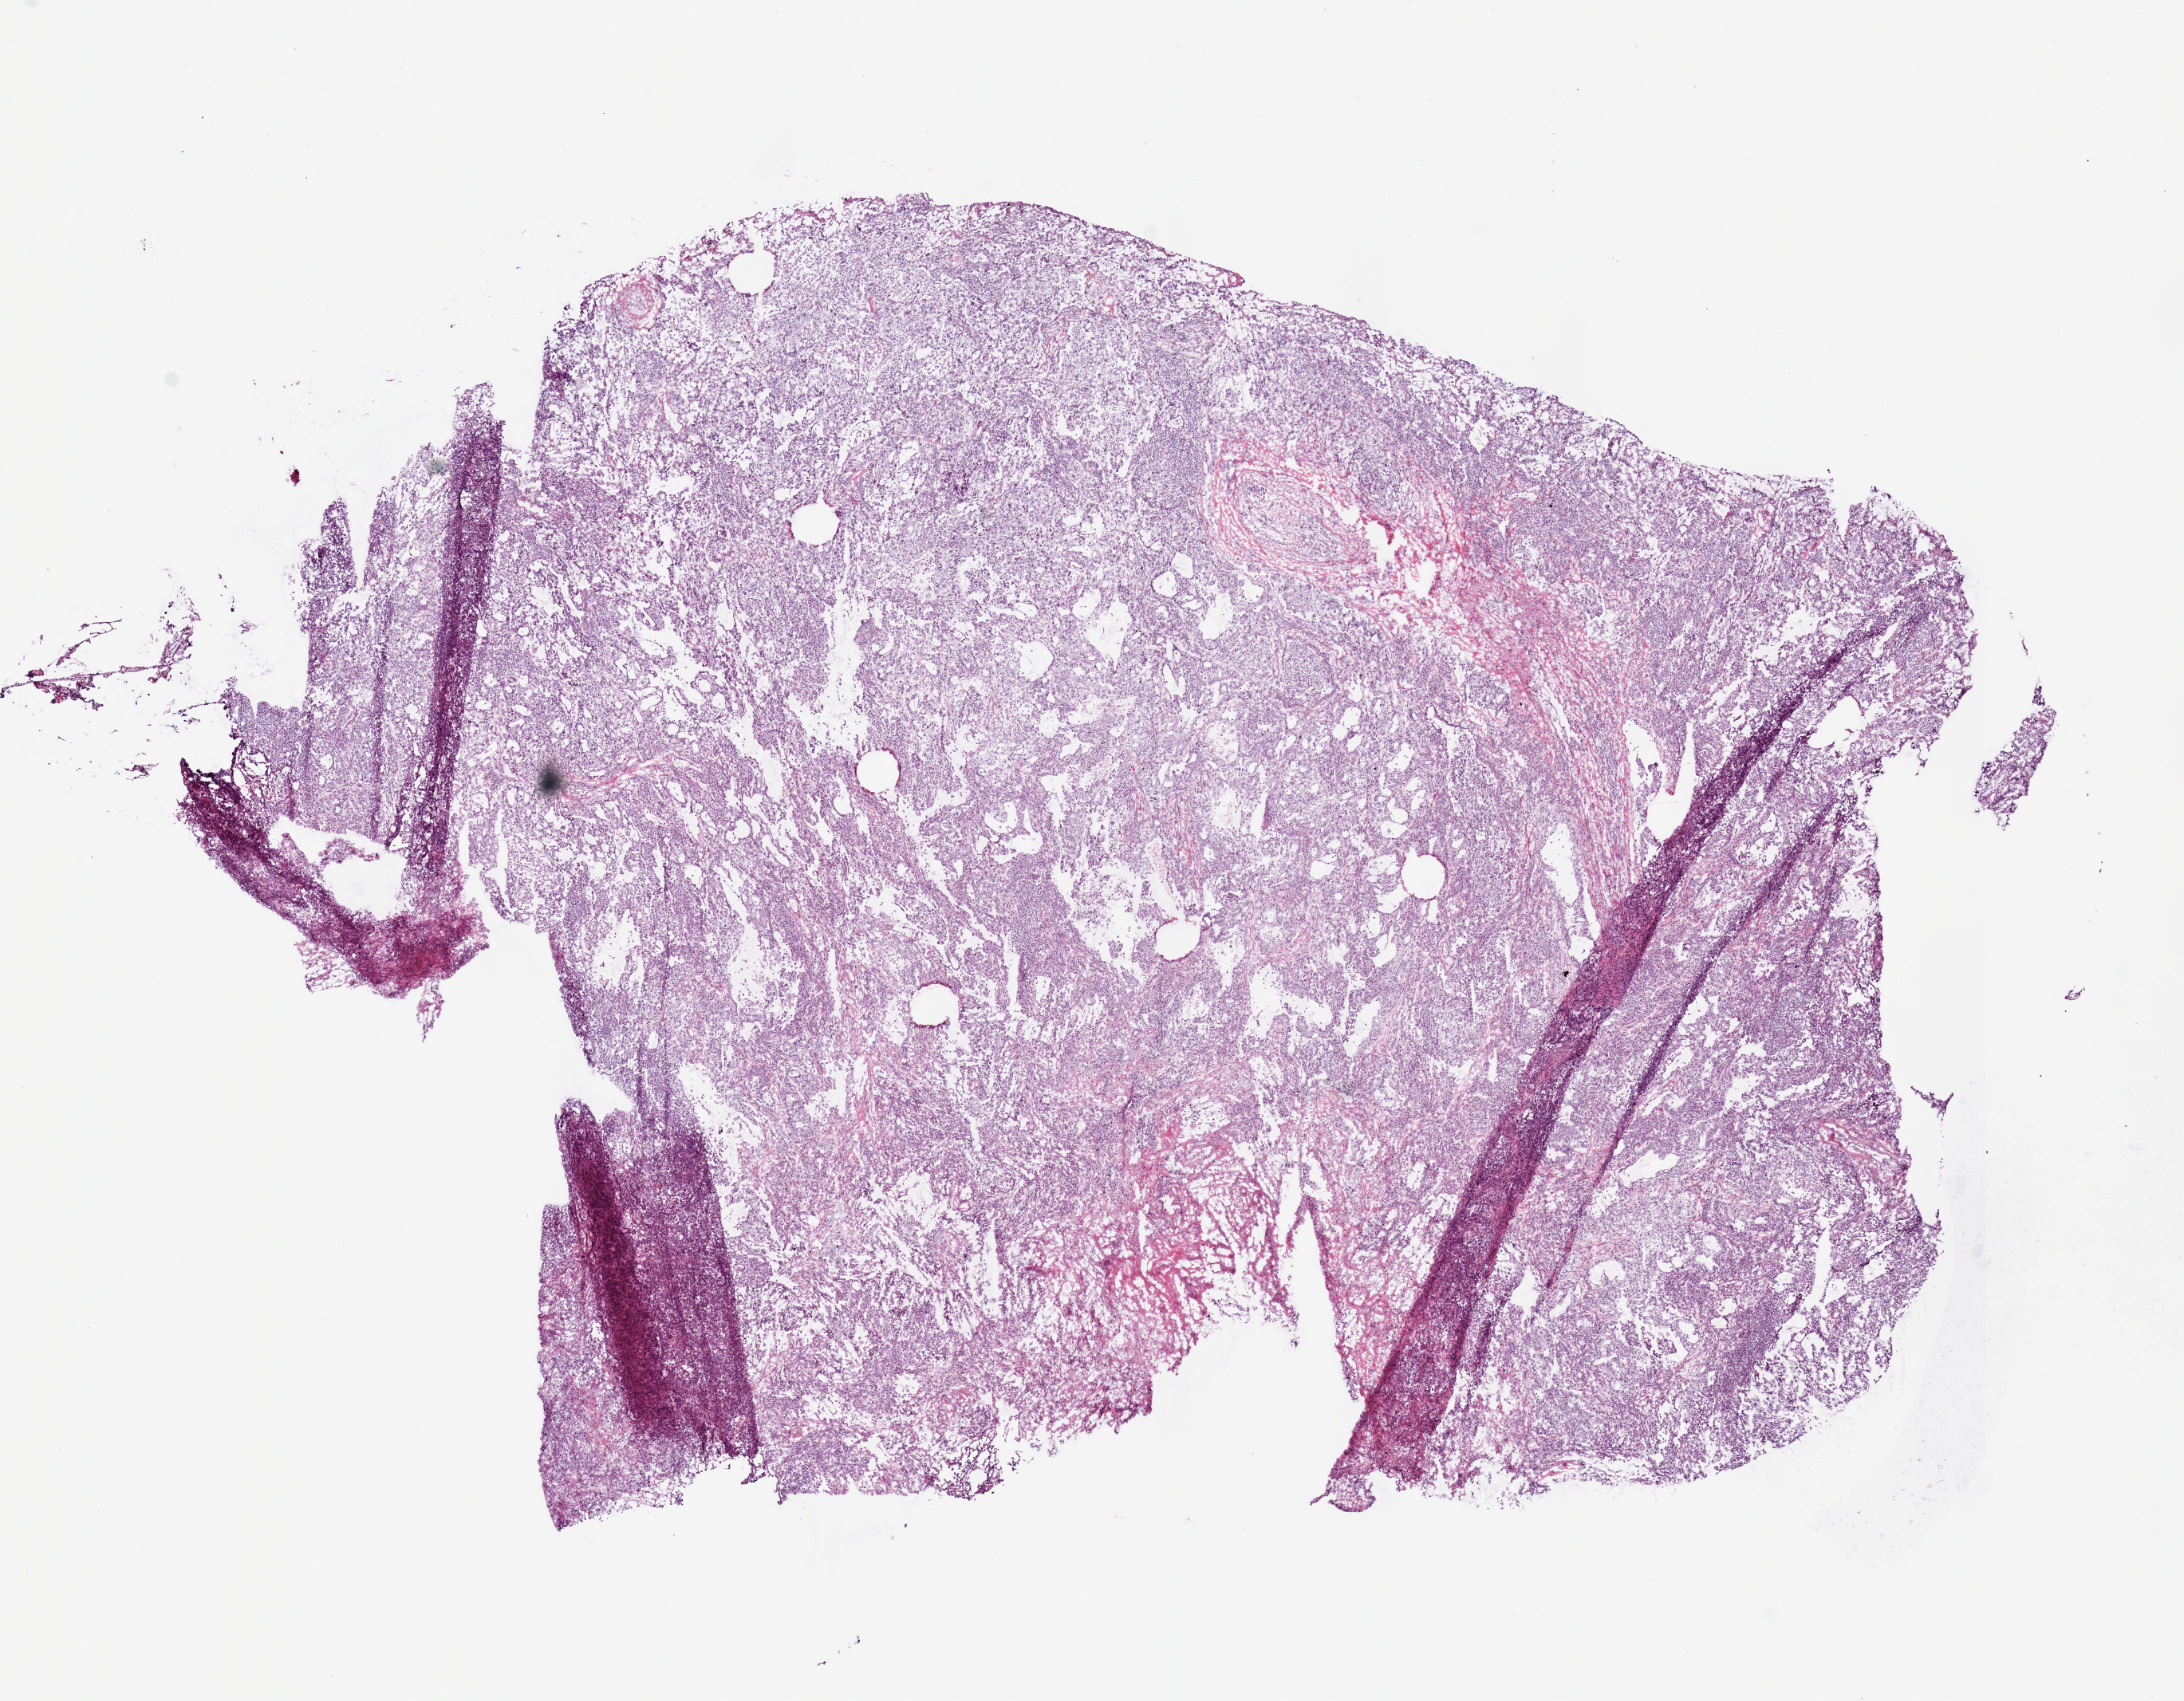
Whole-slide histology image, H&E-stained — shown as a low-resolution overview of the whole scanned area (about 10.8 x 8.4 mm, acquisition: 20x scan). Frozen section from the bottom of the tissue portion. Lung, primary tumour sample. Female patient; age at initial diagnosis 59 years. Slide review estimates, as recorded: tumour cells 95%, tumour nuclei 70%, normal cells 0%, stromal cells 0%, necrosis 5%. Inflammatory infiltration, as recorded: lymphocyte infiltration 20%, monocyte infiltration 1%, neutrophil infiltration 2%.
- pathologic diagnosis: Adenocarcinoma, NOS (lower lobe, lung)
- AJCC pathologic stage: IB (7th edition)